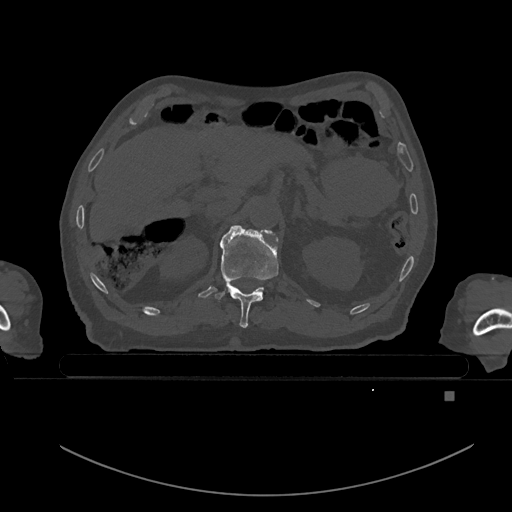
CT including the spine, one axial slice; slice 14 of 969 in the series (ordered by position); bone window (W 1800 / L 400 HU); 0.5 mm slice thickness; 512 × 512 image matrix, field of view 456 × 456 mm. Male patient, age 82 years. Case-level facts recorded for this patient, not image findings: primary cancer: prostate; vertebrae with lytic lesions (as recorded): T11, T9, T8, T2.
Outlined on this slice (semi-automatic segmentation, software-assisted and operator-edited):
- T11 vertebra: box from (x=214, y=227) to (x=279, y=328) px